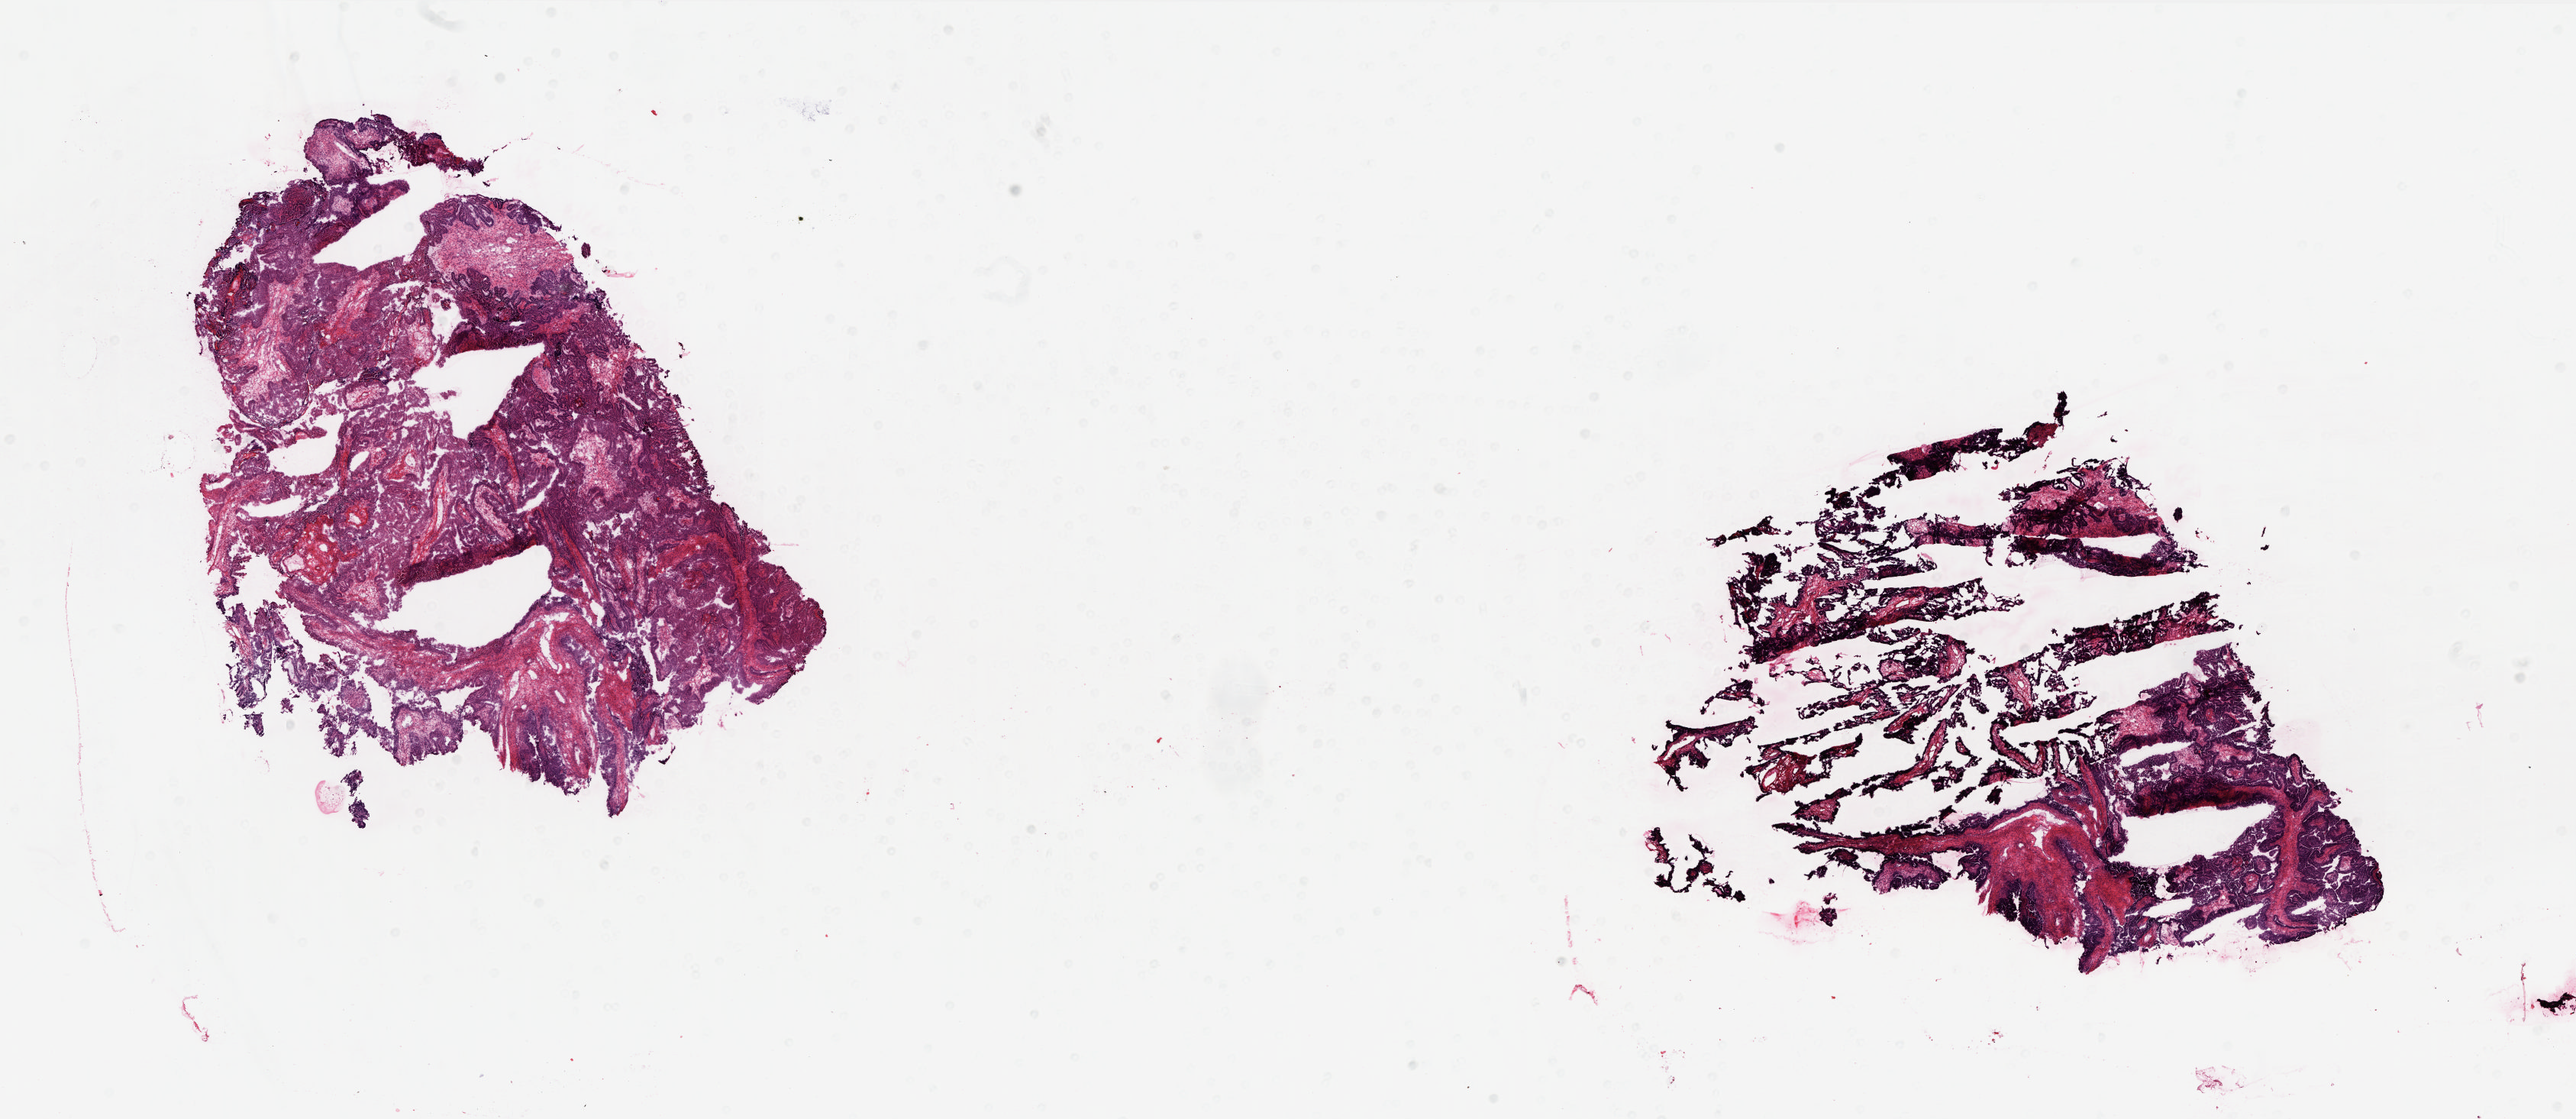
Whole-slide histology image, Hematoxylin and eosin (H&E) stained, a low-resolution overview of the entire scanned area, about 26.9 x 11.7 mm (from a 20x scan), frozen section from the top of the tissue portion, primary tumour sample from the ovary. Female patient; age at initial diagnosis 45 years. Histologic grade: G2 (moderately differentiated). Pathologist review of this section (percent, as recorded): tumour cells 85%, tumour nuclei 95%, normal cells 0%, stromal cells 10%, necrosis 5%.
• laterality: bilateral
• diagnosis: Serous cystadenocarcinoma, NOS
• FIGO stage: IIIA